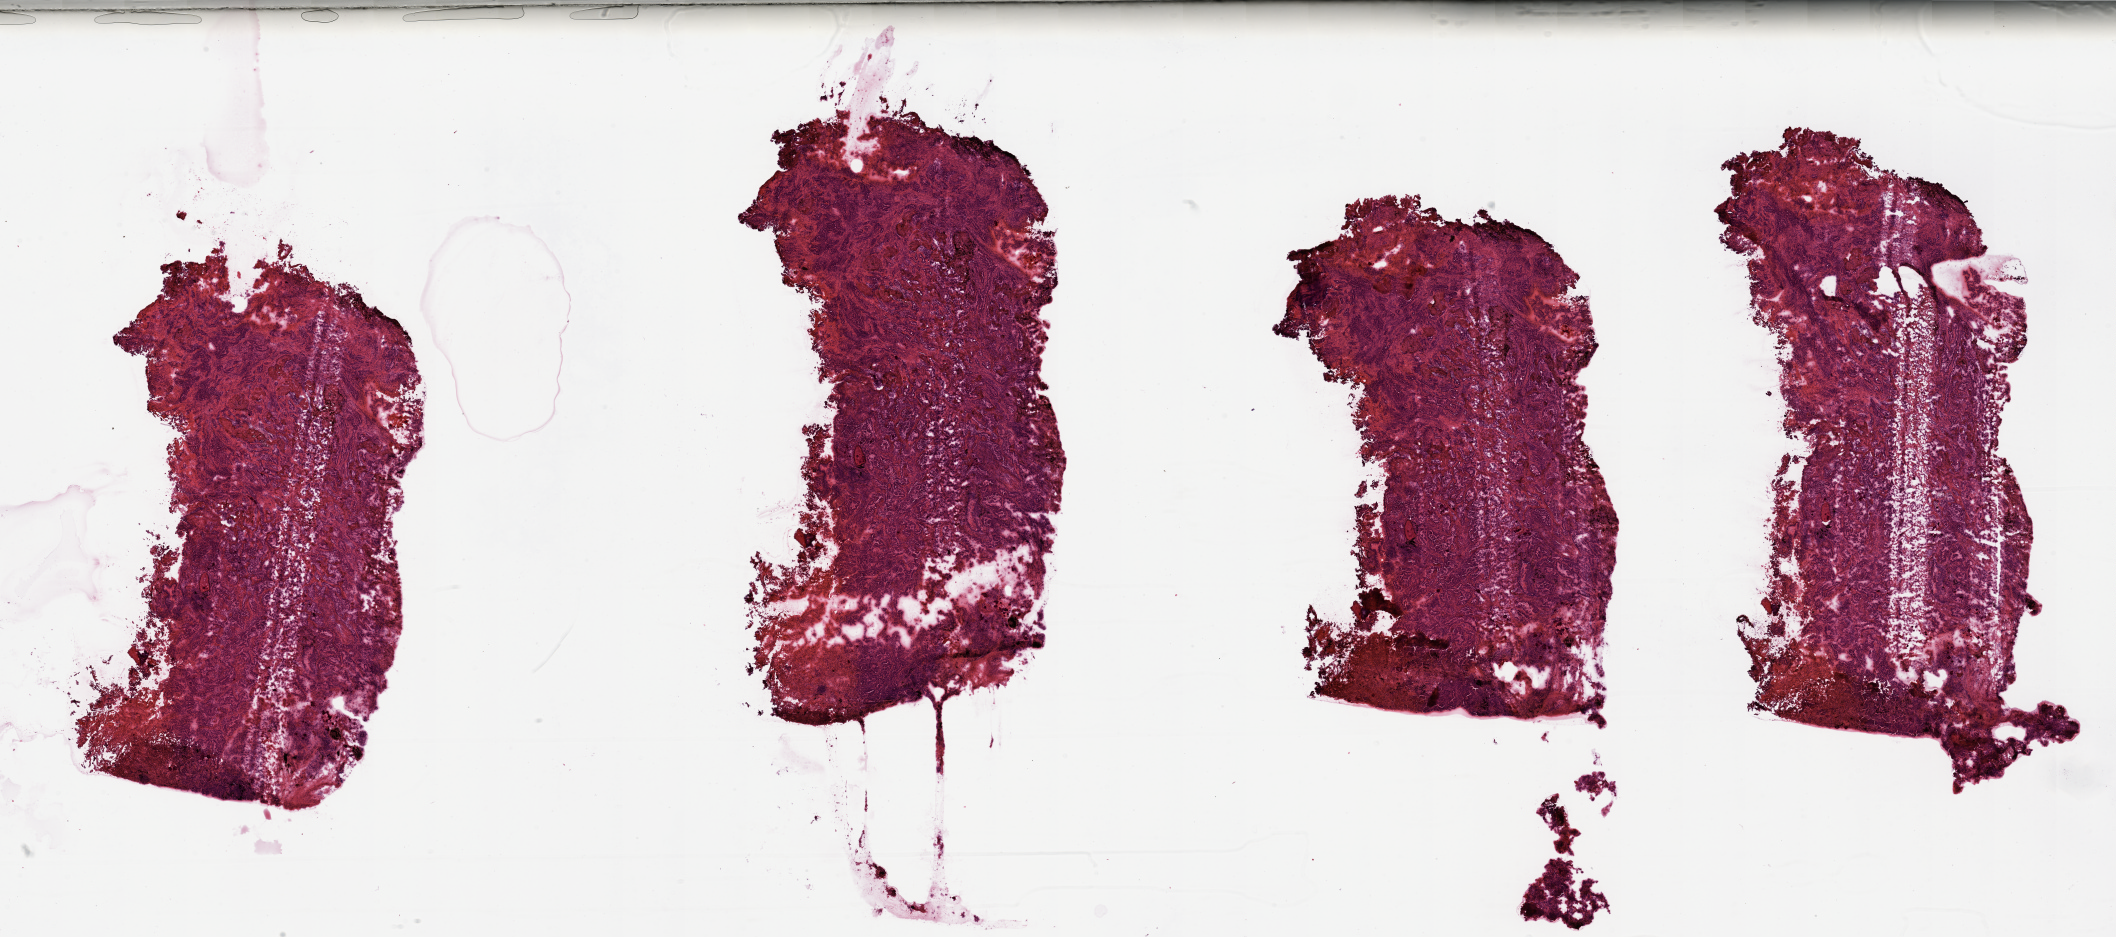
Digitized H&E-stained tissue section (whole slide) — shown as a low-resolution overview of the whole scanned area (about 33.5 x 14.8 mm, from a 20x scan), lung, tumour tissue. 73-year-old male patient. Histologic grade: GX (grade cannot be assessed).
Histologic diagnosis: Adenocarcinoma, NOS. Primary tumour site (as recorded): right upper lobe. AJCC pathologic stage: IB.